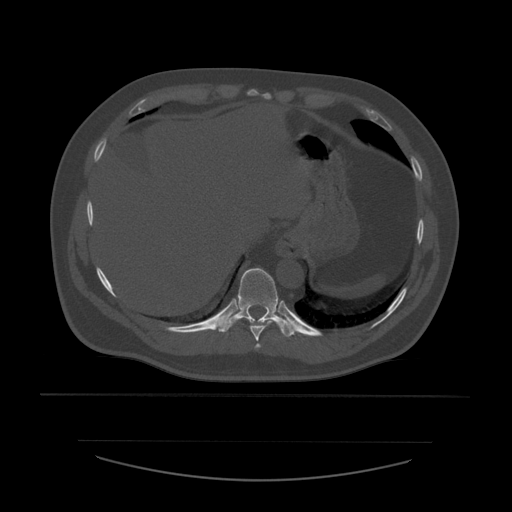
CT including the spine, one axial slice; slice 305 of 532 in the series (ordered by position); reconstruction kernel STANDARD; bone window (W 1800 / L 400 HU); 512 × 512 image matrix. Patient age 44 years. Case-level facts recorded for this patient, not image findings: primary cancer: soft tissue sarcoma.
Annotated regions visible in this slice (semi-automatically segmented with operator editing):
- T10 vertebra: bounding box (x1, y1, x2, y2) in pixels: (215, 268, 299, 338)
- T8 vertebra: (255, 344, 261, 349)
- T9 vertebra: (250, 320, 277, 342)